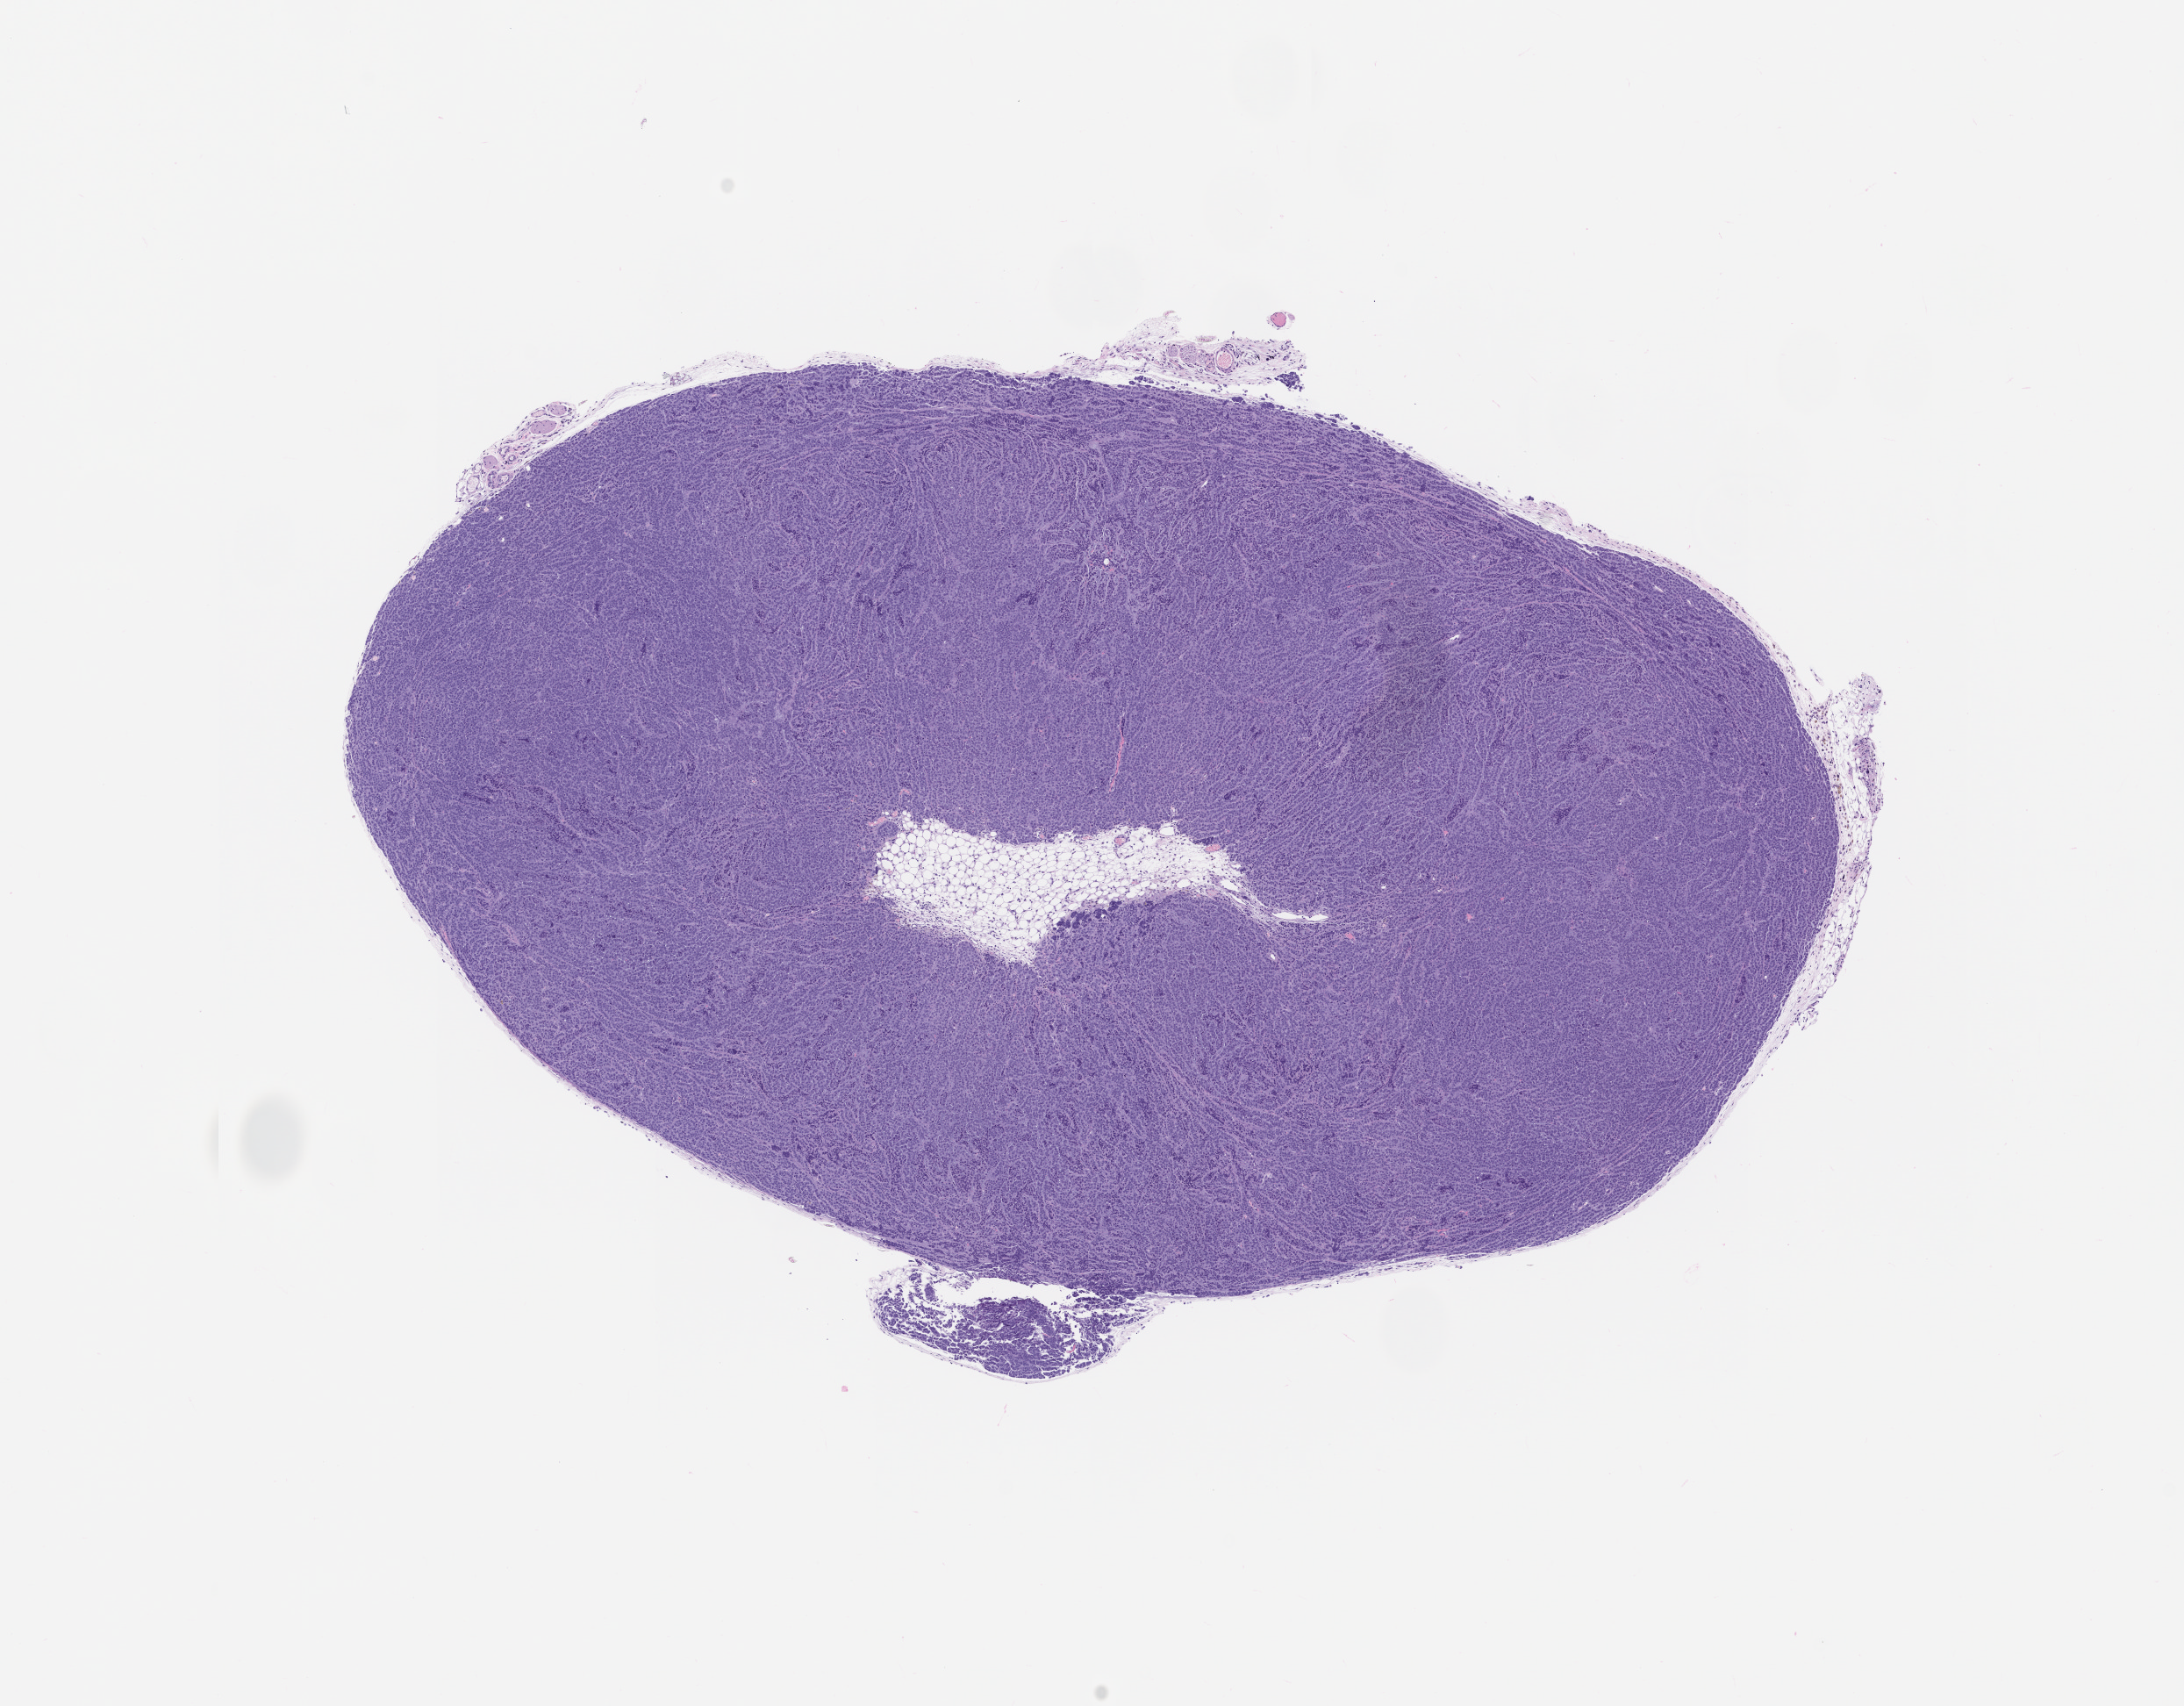
H&E whole-slide image of a patient-derived xenograft (PDX) tumor grown in a mouse, passage 1 — shown as a low-resolution overview of the whole scanned area (about 10.0 x 7.8 mm), formalin-fixed paraffin-embedded section, tumor site category: ovary.
Originating patient diagnosis: Ovarian Carcinoma.